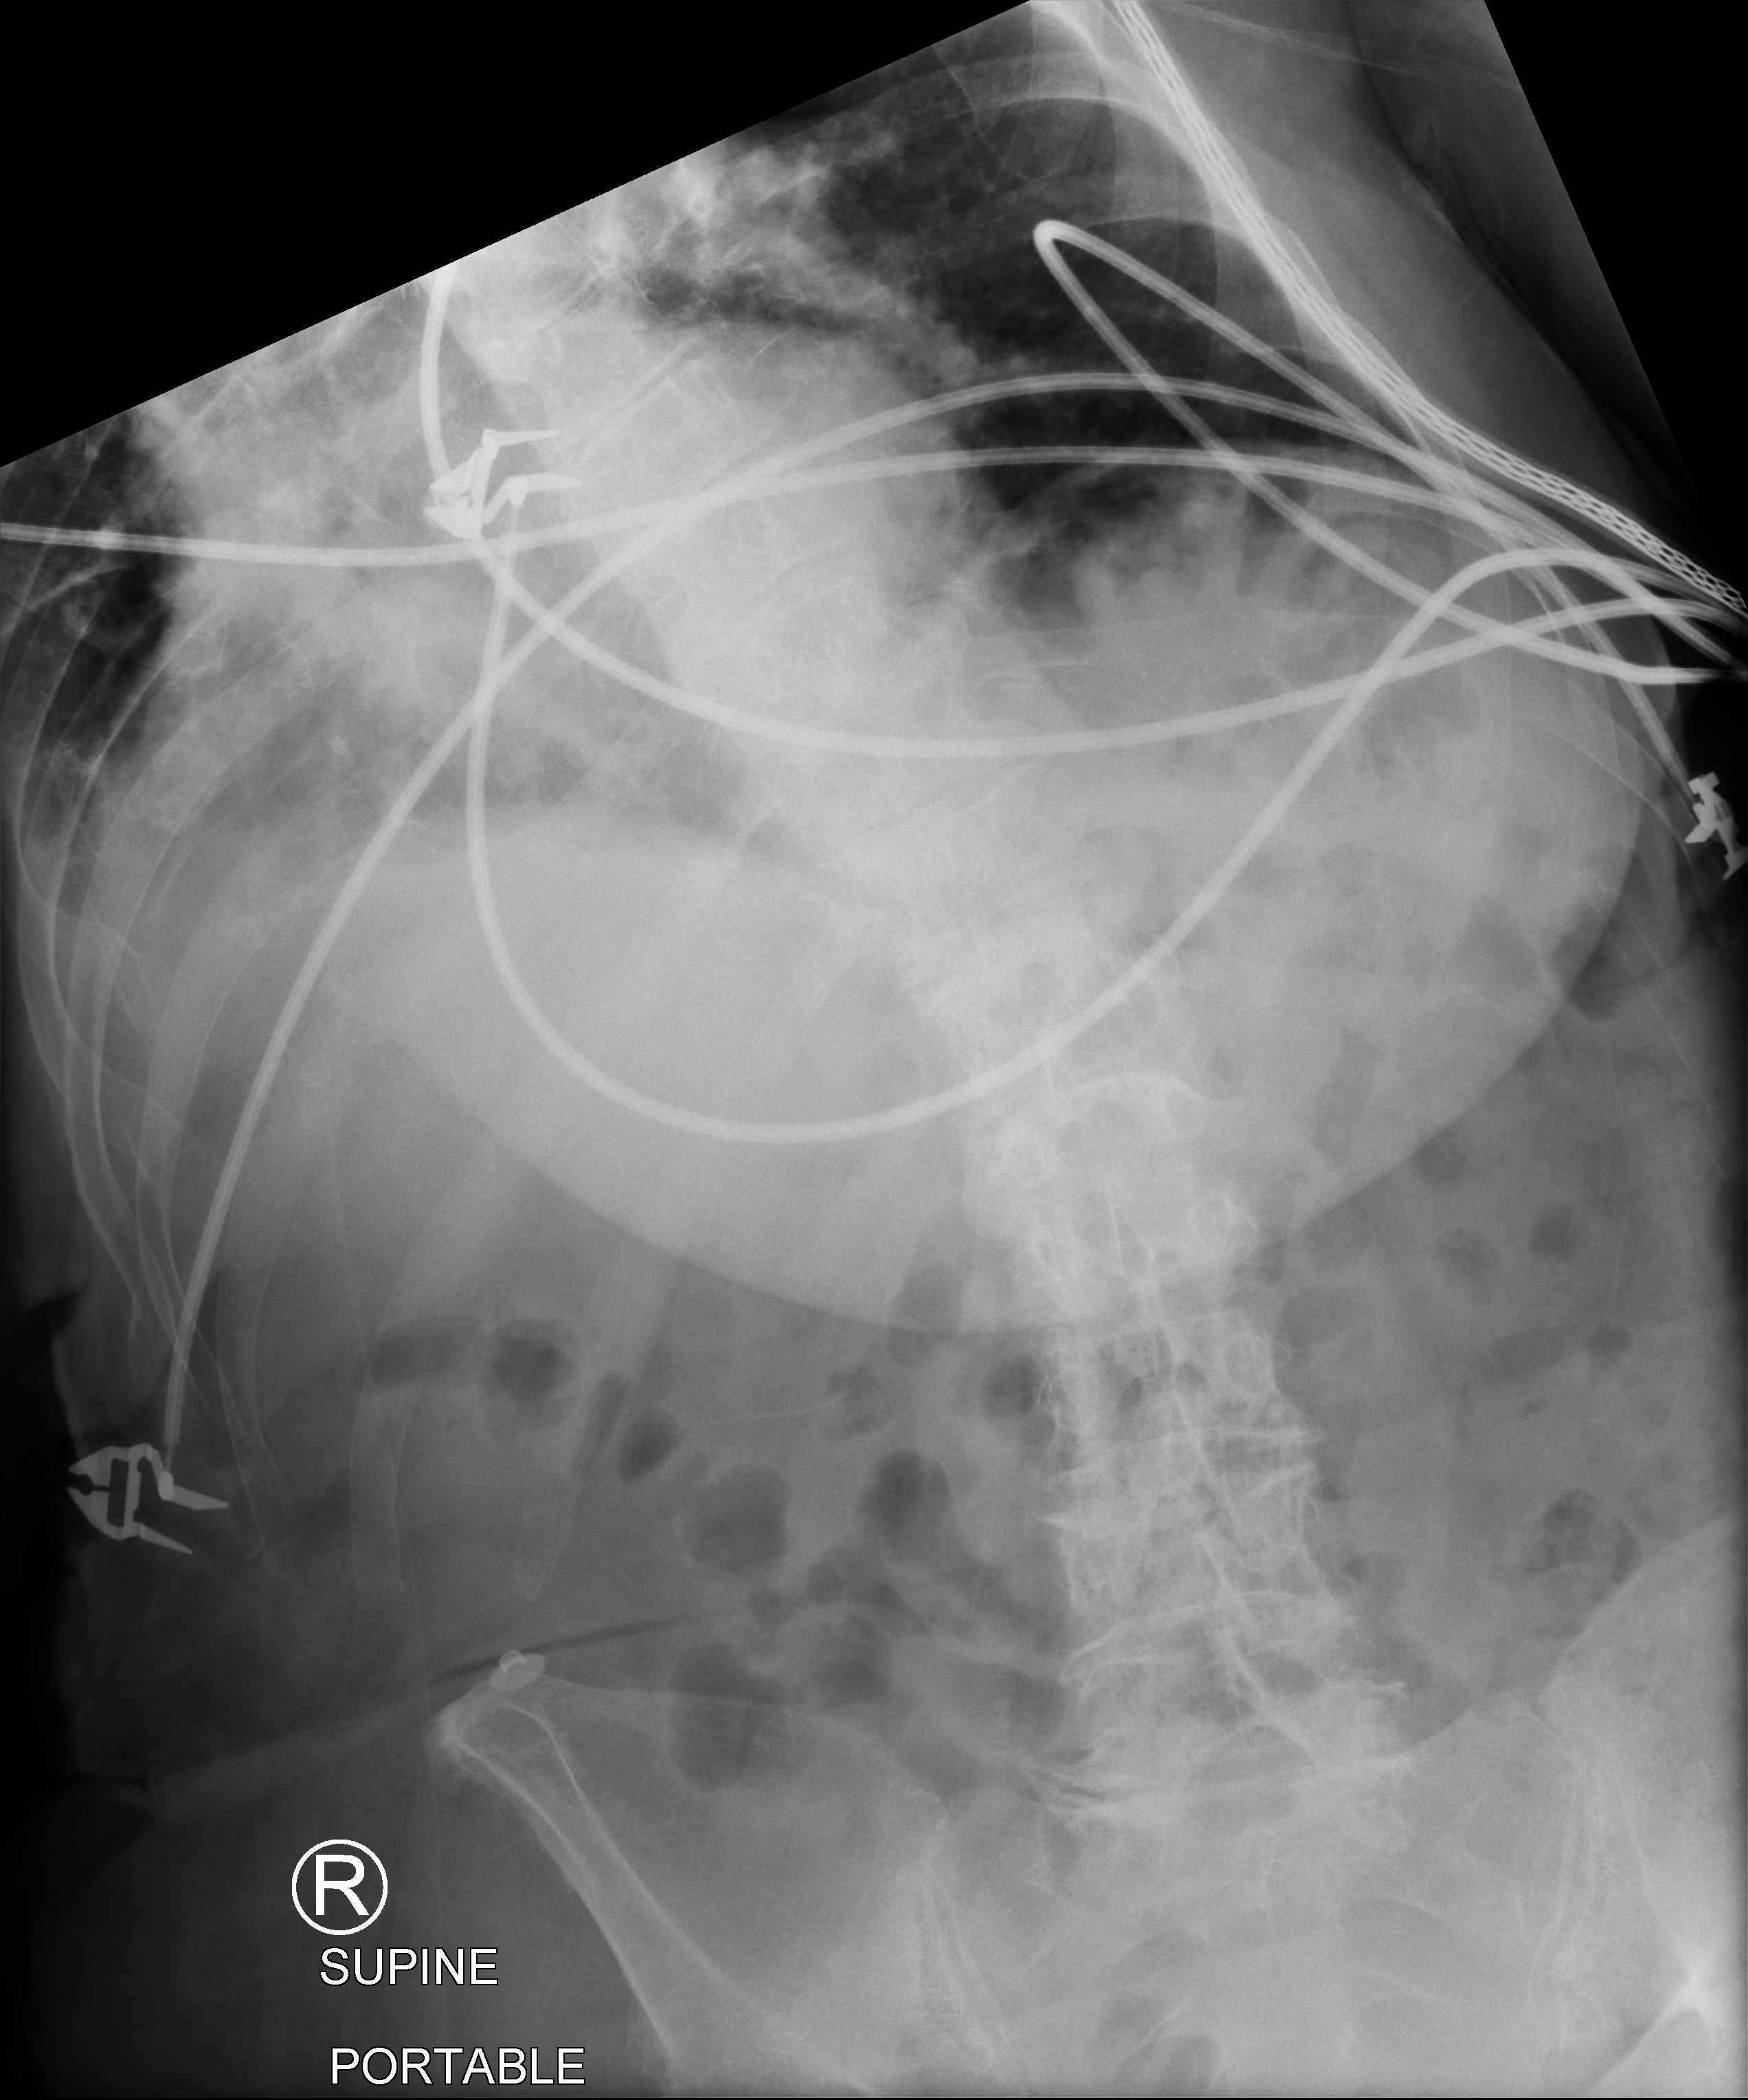
Bedside abdomen radiograph (computed radiography); anteroposterior (AP) projection. Female patient hospitalised with COVID-19, age 75–90 years.
Hospital-stay facts (about this admission, not read from this image; timing relative to this image not recorded):
- mechanically ventilated during this hospital stay: no
- chronic kidney disease (admission record): no